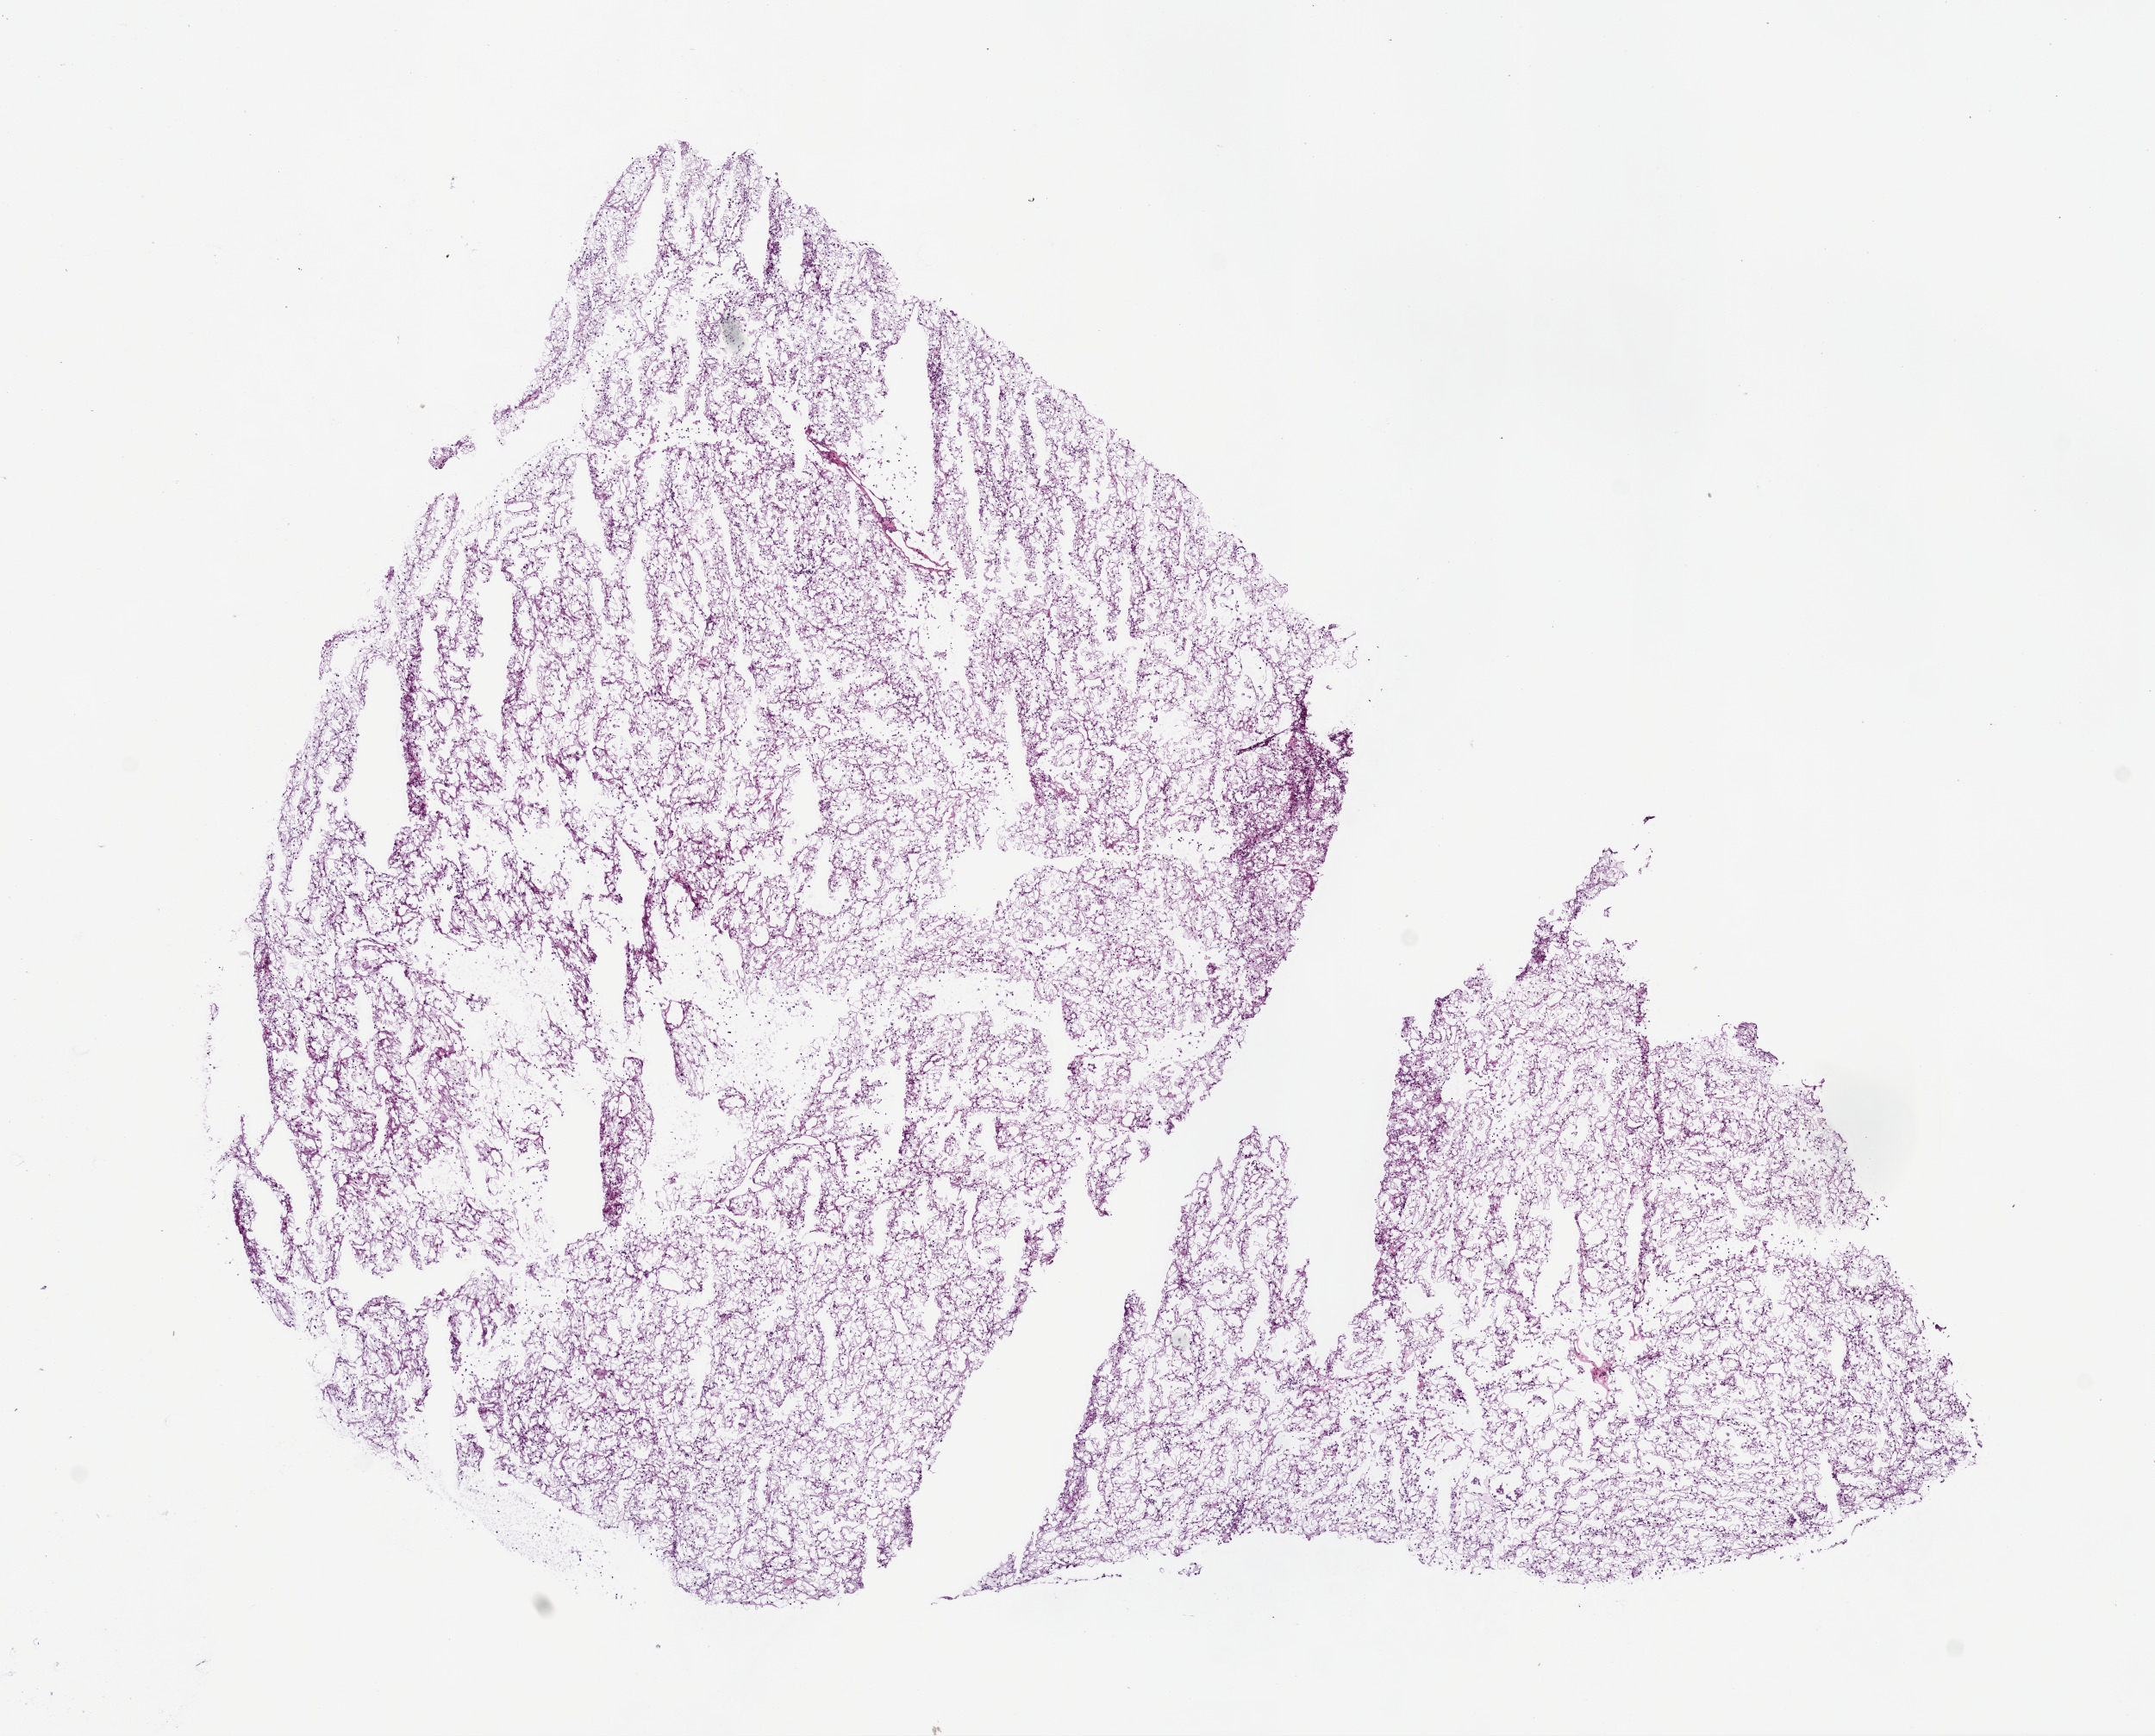
Whole-slide histology image, Hematoxylin and eosin (H&E) stained, shown as a low-resolution overview of the whole scanned area (about 10.0 x 8.1 mm, from a 20x scan), frozen section, primary tumour sample from the kidney. Patient: male, age at initial diagnosis 79 years. Histologic grade: G2 (moderately differentiated). Composition of this section per pathologist review: tumour cells 95%, tumour nuclei 90%, normal cells 0%, stromal cells 5%, necrosis 0%.
AJCC pathologic stage: III. Laterality: left. Lymph nodes positive (case pathology): 0 of 1 examined. Histologic diagnosis: Clear cell adenocarcinoma, NOS.